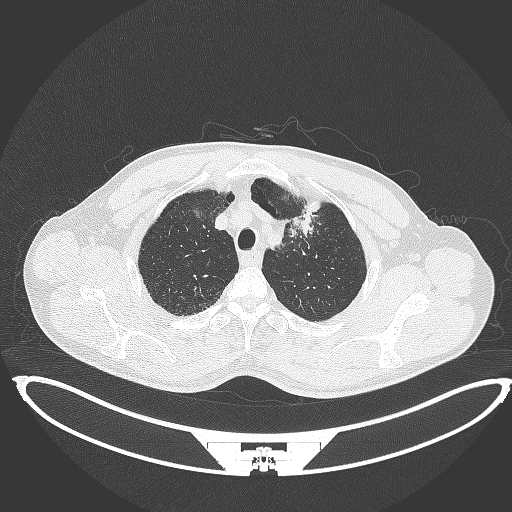
Chest CT, one axial slice. Slice 368 of 395 in the series (ordered by position). Reconstruction kernel B70f. 120 kVp. Lung window (W 1500 / L -600 HU). 1 mm slice thickness. 512 × 512 image matrix. Patient: male, 60 years. From the clinical record (not read from this slice): clinical TNM (as recorded): T2a N0 M0; histopathological grade: G1-G2.
Annotated regions visible in this slice (bounding box drawn by a radiologist):
- lung tumour (recorded histology: squamous cell carcinoma): bounding box <285,211,315,241> (left, top, right, bottom; pixels)